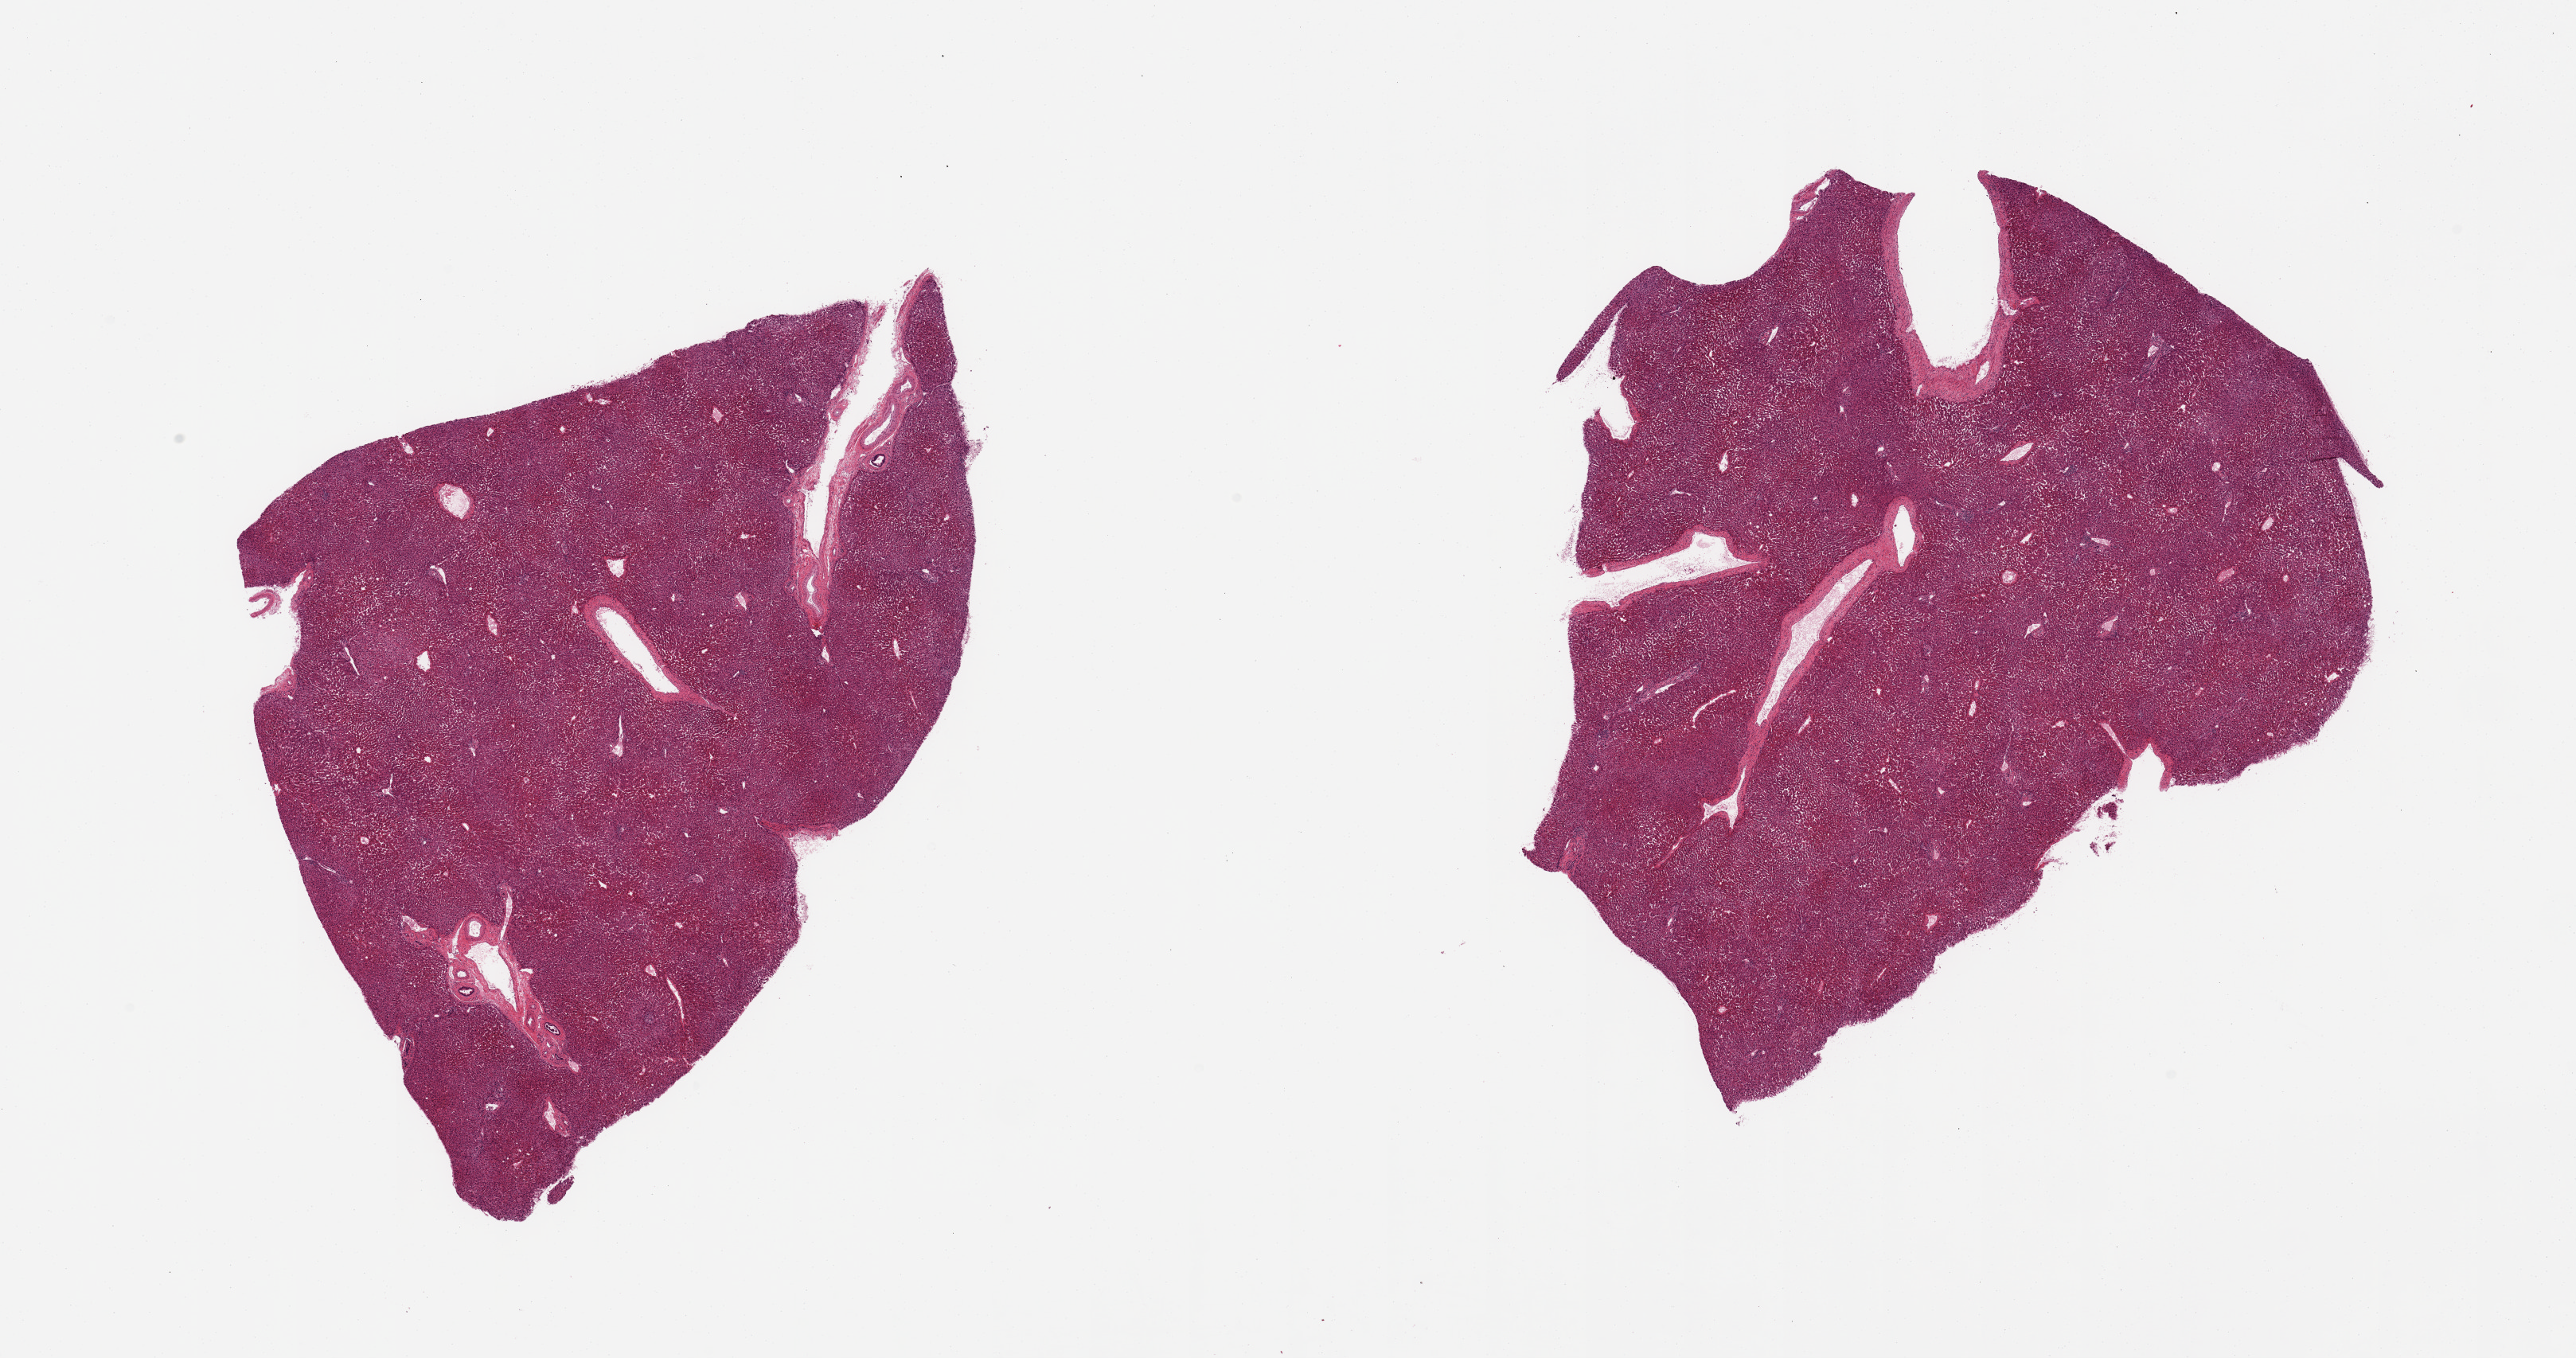
Whole-slide image, H&E stain — shown as a low-resolution overview of the whole scanned area (about 25.6 x 13.5 mm, slide scanned at 20x); PAXgene-fixed paraffin-embedded (PFPE) section; target tissue: liver; tissue donor sample.
Pathologist's review note for this sample: 2 pieces; mild steatosis.